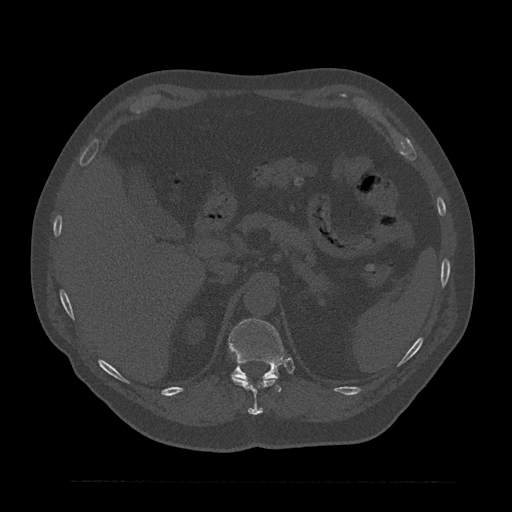
CT including the spine, one axial slice. Slice 259 of 797 in the series (ordered by position). Reconstruction kernel Br40s/3. 120 kVp. Bone window (W 1800 / L 400 HU). 0.5 mm slice thickness. 512 × 512 image matrix, field of view 430 × 430 mm. Male patient, age 61 years. From the clinical record (not read from this slice): primary cancer: prostate.
Annotated regions visible in this slice (semi-automatic segmentation, software-assisted and operator-edited):
- T11 vertebra: box from (x=231, y=375) to (x=277, y=415) px
- T12 vertebra: (x=229, y=318)–(x=284, y=392)